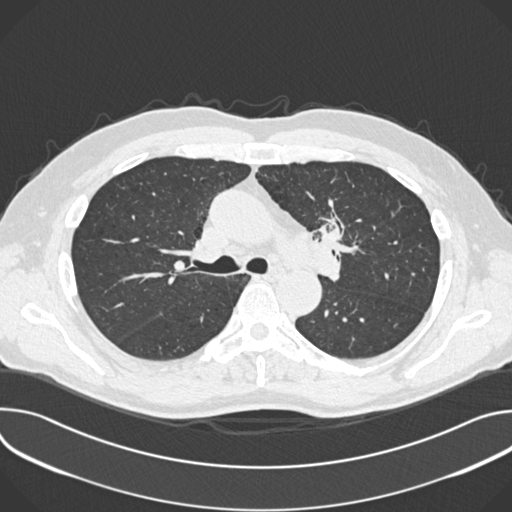
Low-dose screening chest CT, one axial slice. Position 246 of 361 along the scan axis. 120 kVp. Lung window (W 1500 / L -600 HU). 1 mm slice thickness. 512 × 512 image matrix.
Annotated regions visible in this slice (manually delineated by an expert):
- lesion 1 (tumor, upper lobe of left lung): bounding box [x1, y1, x2, y2] px = [319, 219, 344, 248]